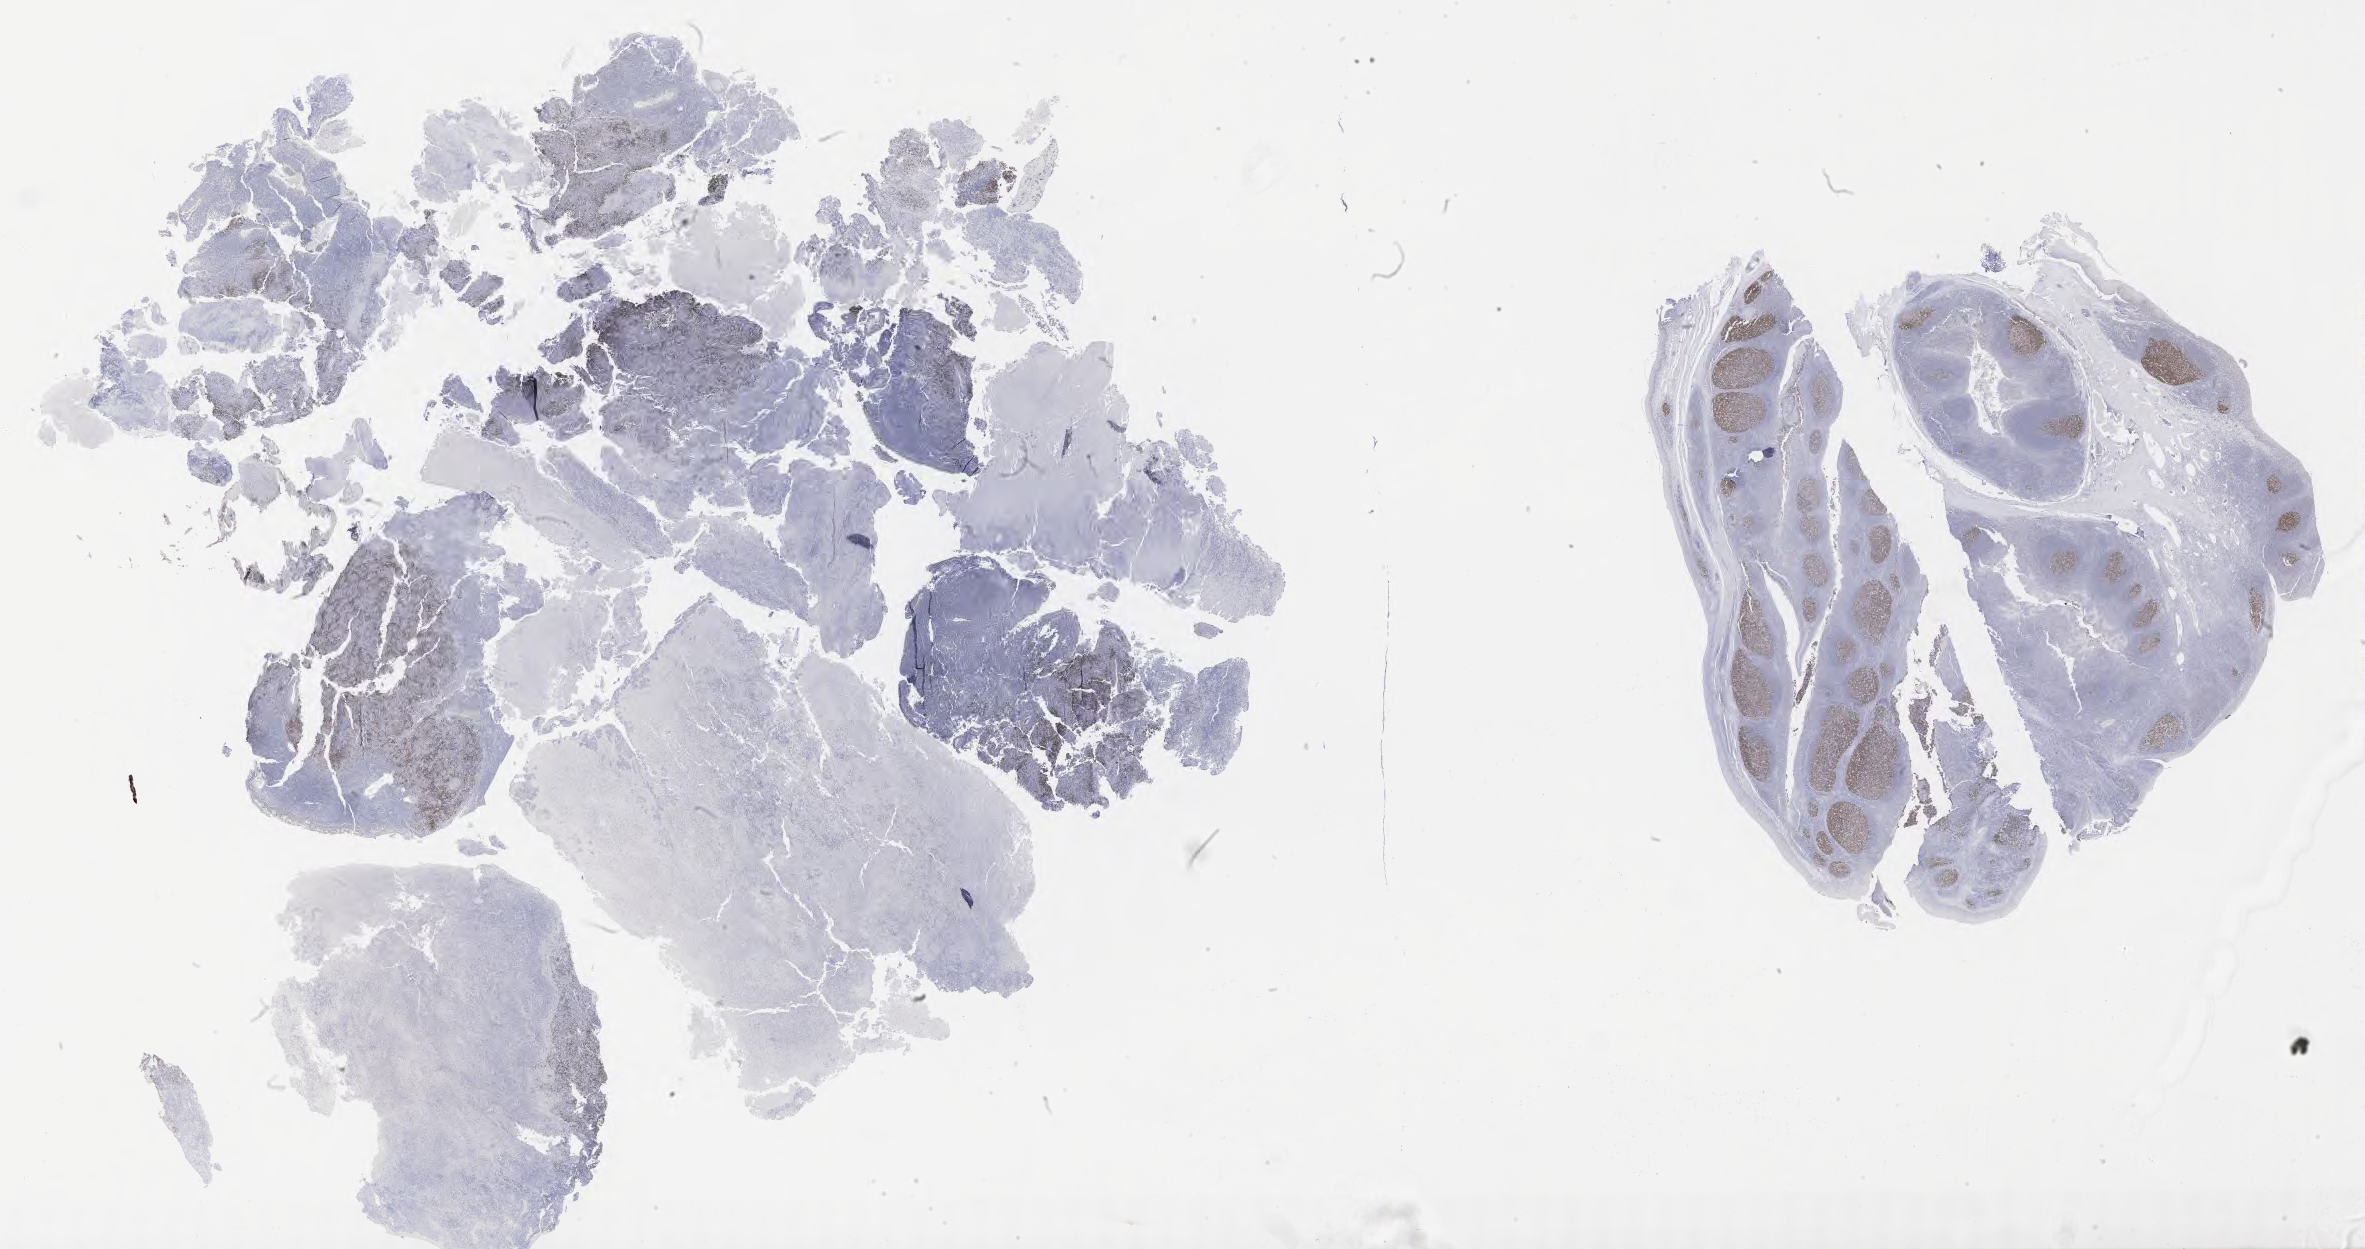
Immunohistochemistry (IHC) whole-slide image stained for BCL6, low-resolution overview of the scanned area, about 38.2 x 20.2 mm. Specimen: tumor tissue. Patient male; aged 47.
* diagnosis: Diffuse large B-cell lymphoma, NOS